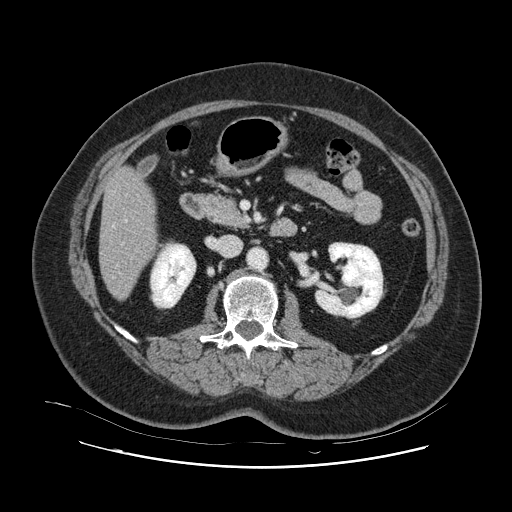
Contrast-enhanced abdominal CT, one axial slice; position 34 of 132 along the scan axis; intravenous contrast given; soft-tissue window (W 400 / L 40 HU); 2.5 mm slice thickness; 512 × 512 image matrix. Female patient, age 73 years. From the clinical record (not read from this slice): diagnosis: colorectal cancer liver metastases, imaged before liver resection; multiple liver metastases: no; largest metastasis: 7 cm; disease in both lobes: no.
Annotated regions visible in this slice (expert manual segmentation):
- hepatic veins: bounding box [x1, y1, x2, y2] px = [113, 224, 115, 227]
- liver: [100, 168, 156, 299]
- planned liver remnant (the part of the liver to remain after resection): [100, 168, 156, 300]